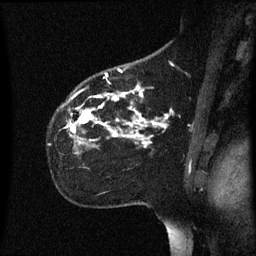
Breast MRI (dynamic contrast-enhanced), one sagittal slice. Dynamic contrast-enhanced series, image 2 of 3 at this slice position (ordered by acquisition). 1.5 T. TE 4.2 ms, TR 8.4 ms. 256 × 256 image matrix. Female patient, age 35 years. From the clinical record (not read from this slice): setting: breast cancer imaged before/during neoadjuvant chemotherapy; receptor status: HER2-positive.
Outlined on this slice (semi-automatic segmentation, software-assisted and operator-edited):
- analysis volume of interest (the breast-tissue region the enhancement analysis was run in; not a lesion): bounding box (x1, y1, x2, y2) in pixels: (50, 78, 173, 155)
- tumour enhancement mask (voxels above the 70 % enhancement threshold inside the analysis volume of interest): (66, 86, 169, 147)